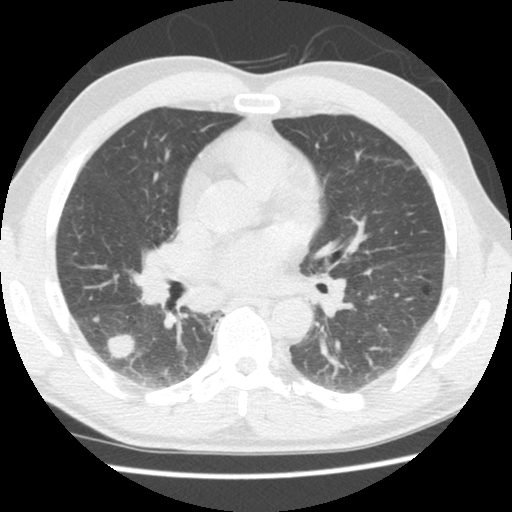
Low-dose screening chest CT, one axial slice. Position 78 of 133 along the scan axis. Reconstruction kernel STANDARD. 140 kVp. Lung window (W 1500 / L -600 HU). 2.5 mm slice thickness. 512 × 512 image matrix, field of view 320 × 320 mm.
Annotated regions visible in this slice (expert manual segmentation):
- lesion 1 (tumor, lower lobe of right lung): bounding box <105,333,136,360> (left, top, right, bottom; pixels)